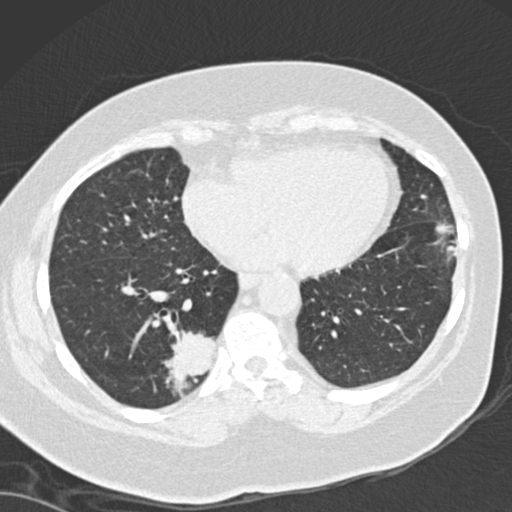
Chest CT (low-dose screening protocol), one axial image. Baseline annual screen. Lung window (W 1500 / L -600 HU). 2 mm slice thickness. Standard (soft-tissue) reconstruction kernel (B30f). Slice 105 of 162 in the series. 512 × 512 image matrix, field of view 328 × 328 mm. Female, age 66 years at enrolment. Current smoker at enrolment.
Expert reader's lesion annotation, bounding box (x1, y1, x2, y2) in pixels: (146, 315, 233, 405). The screening reader recorded 3 non-calcified nodules or masses ≥4 mm on this exam (left lower lobe, left lower lobe, right lower lobe); which of them this box marks is not recorded. Official screen result: positive, change unspecified: nodule(s) >= 4 mm or enlarging nodule(s), mass(es), or other non-specific abnormalities suspicious for lung cancer. Later outcome: lung cancer diagnosed 67 days after this screen — adenocarcinoma, NOS, right lower lobe, well differentiated (G1), stage IB (AJCC 6th edition), 55 mm at pathology.